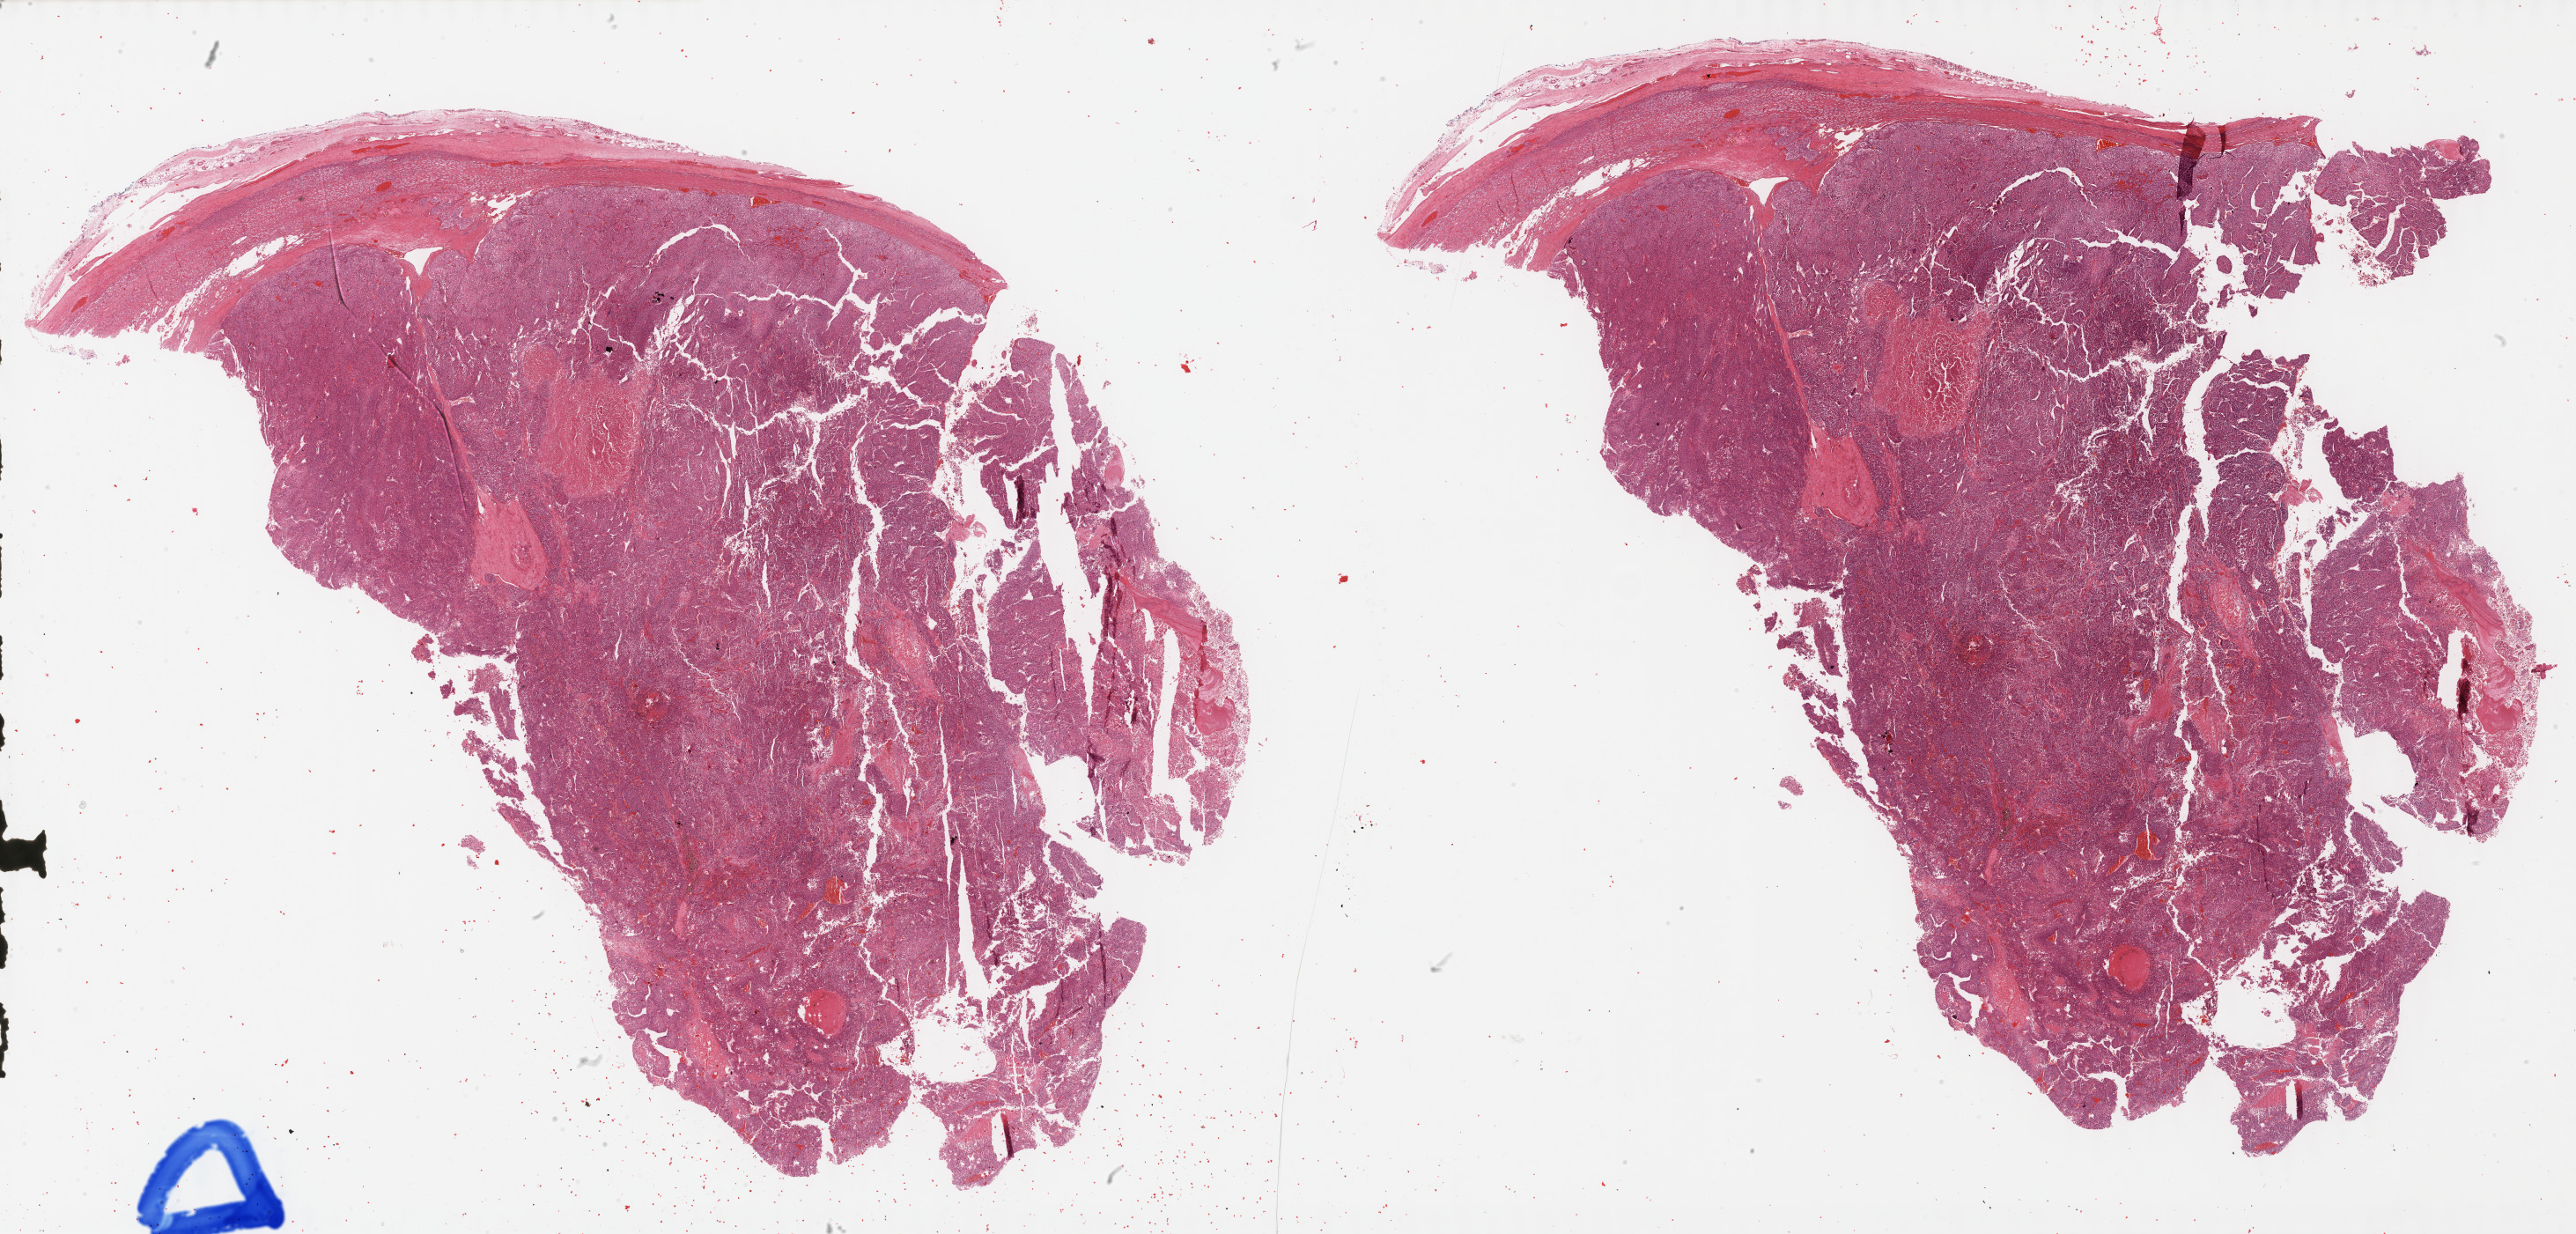
Digitized H&E-stained tissue section (whole slide), a low-resolution overview of the entire scanned area, about 47.3 x 22.6 mm (from a 40x scan); FFPE section; primary tumour sample from the adrenal cortex. Patient: female, age at initial diagnosis 53 years.
Laterality: right. Diagnosis: Adrenal cortical carcinoma (cortex of adrenal gland).